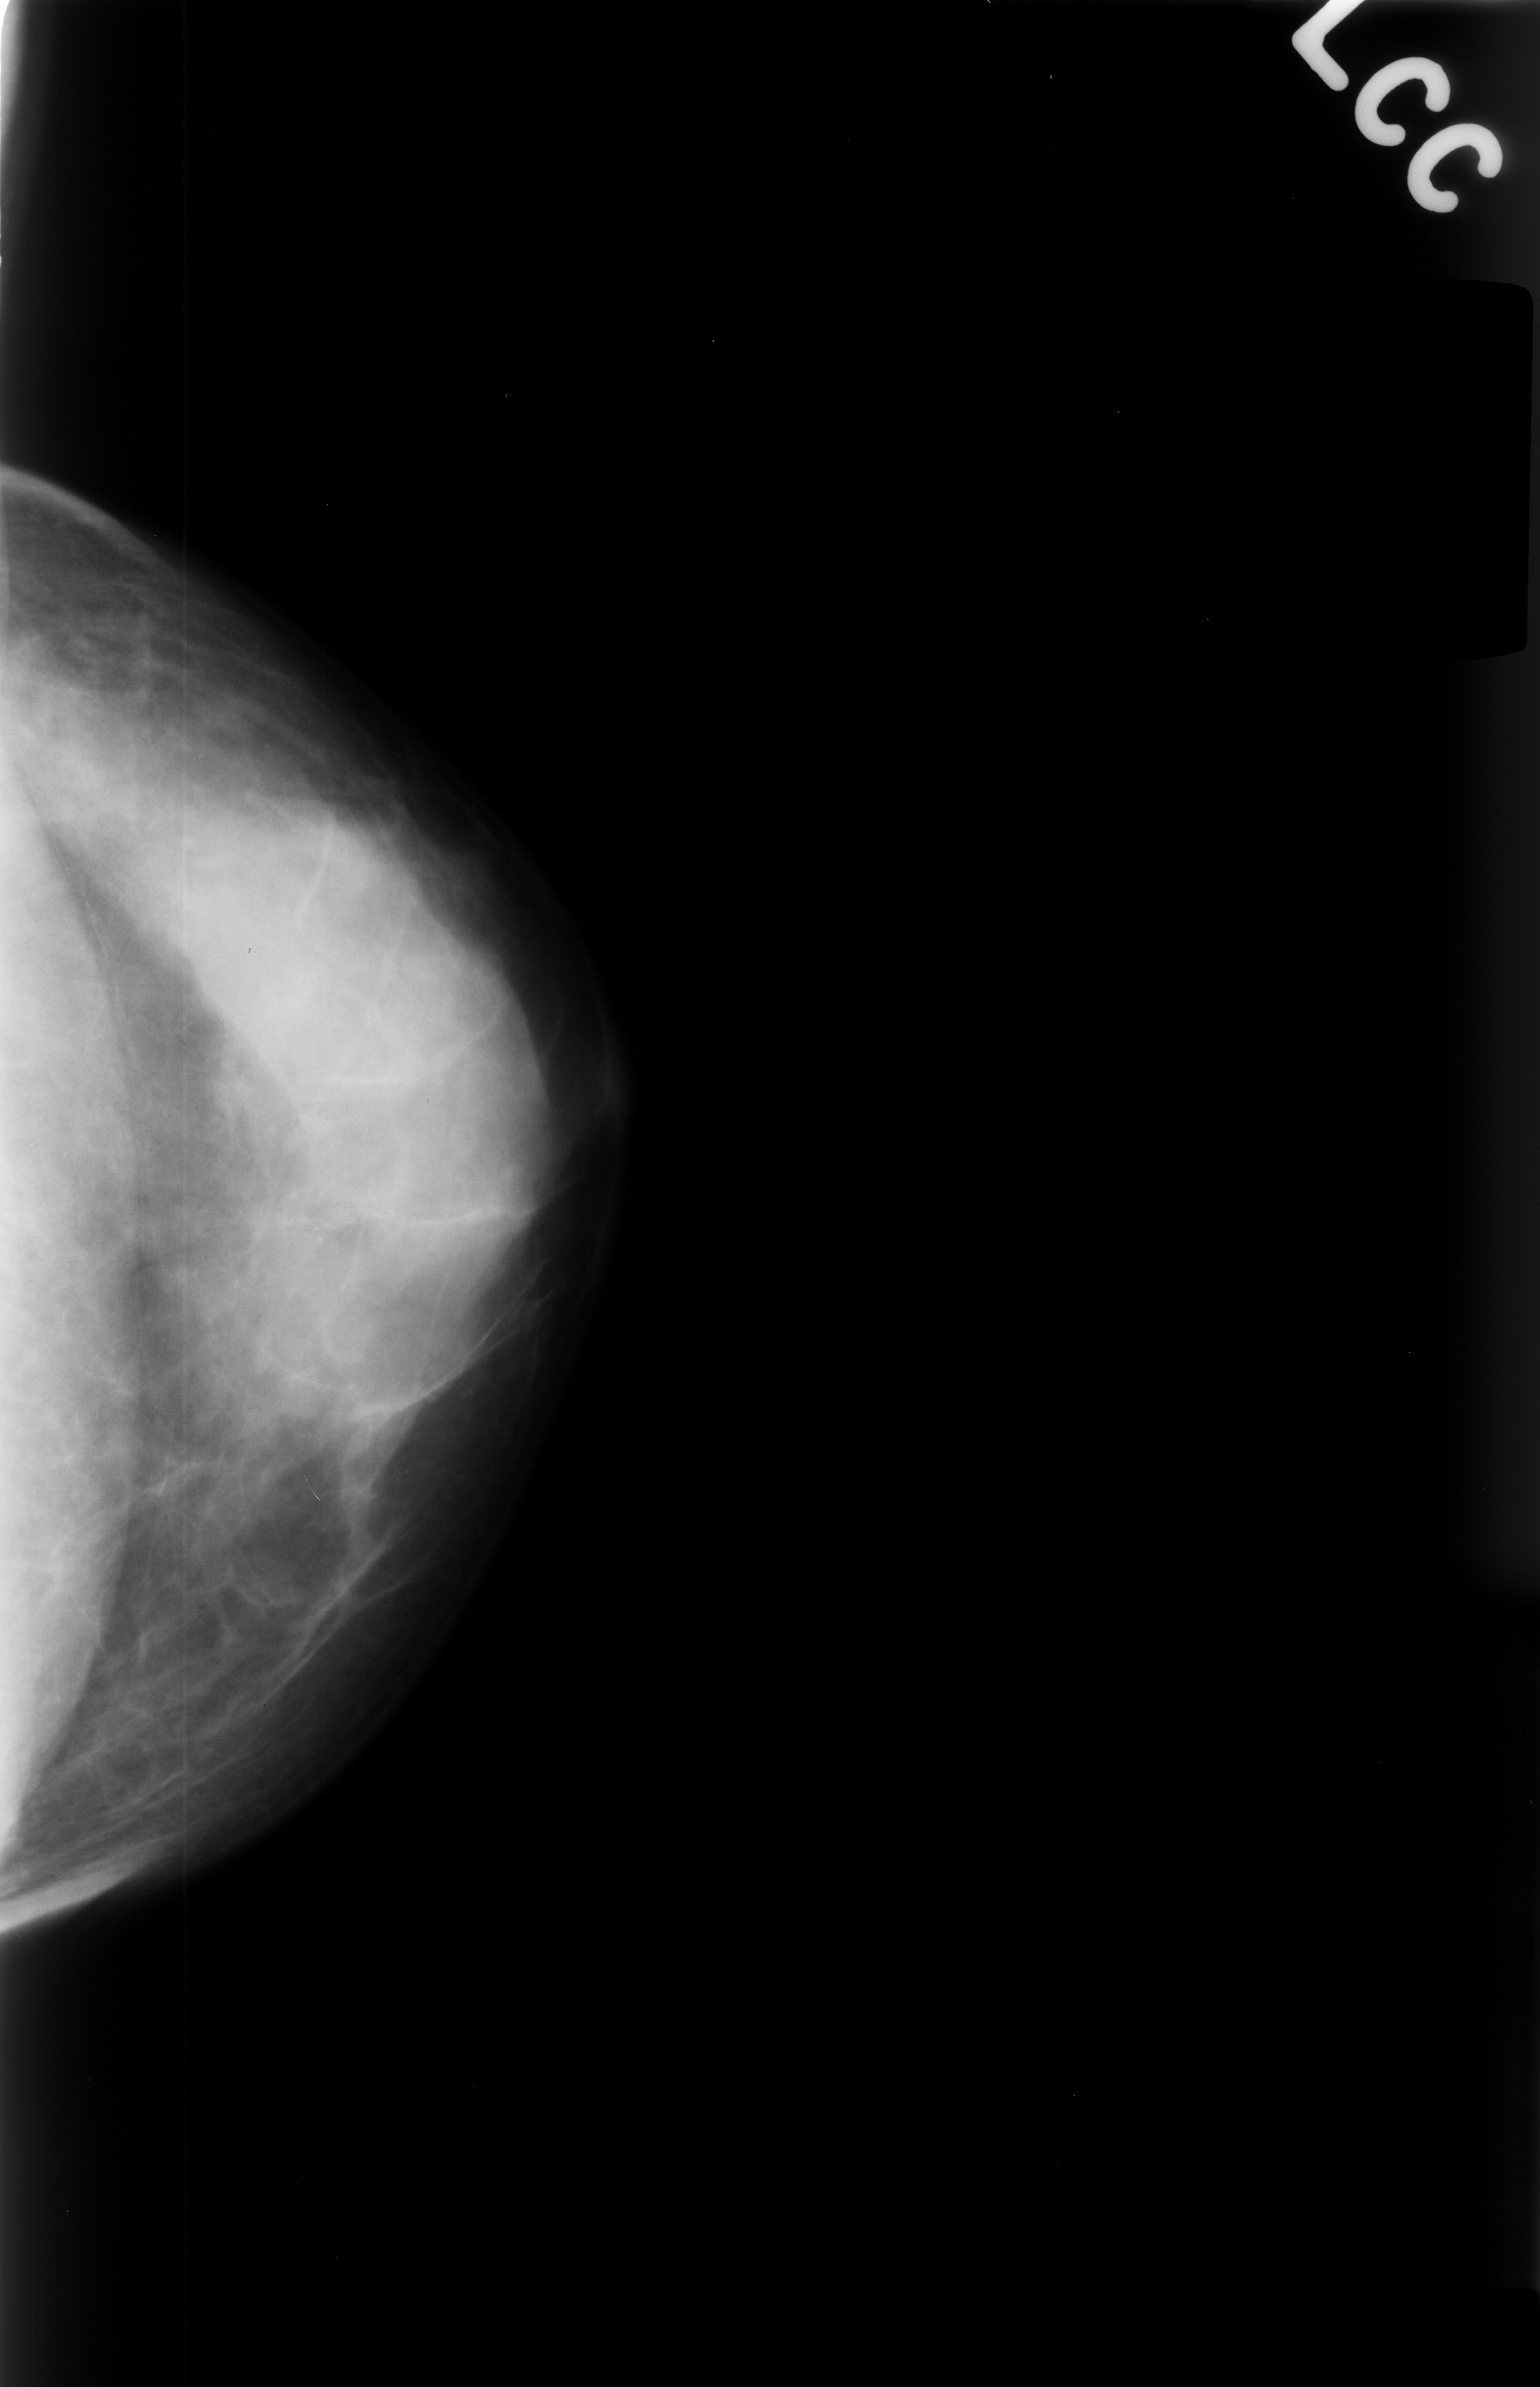
Mammogram (digitized film), left breast, CC view, breast composition: extremely dense (BI-RADS density category 4 of 4).
Calcifications, morphology punctate, distribution clustered; BI-RADS assessment category 4; subtlety rating 3 on a 1 (subtle) to 5 (obvious) scale; pathology result (as recorded, not read from the image): benign.